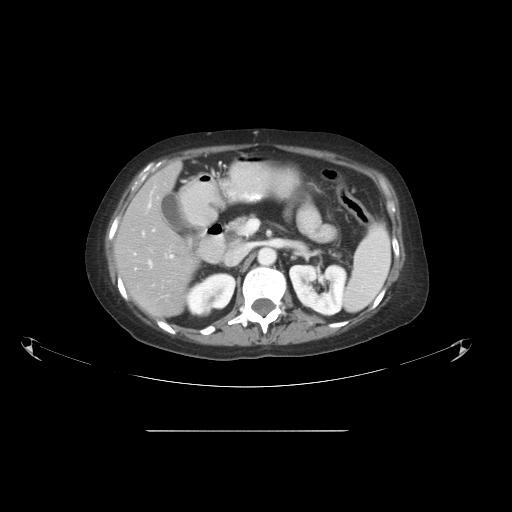
Contrast-enhanced abdominal CT, one axial slice. Slice 29 of 51 in the series (ordered by position). 120 kVp. Intravenous contrast given. Soft-tissue window (W 400 / L 40 HU). 5 mm slice thickness. 512 × 512 image matrix, field of view 475 × 475 mm. Female patient, age 48 years. From the clinical record (not read from this slice): diagnosis: colorectal cancer liver metastases, imaged before liver resection; multiple liver metastases: yes; largest metastasis: 1 cm.
Structures marked on this image (expert manual segmentation):
- hepatic veins: bounding box (x1, y1, x2, y2) in pixels: (148, 198, 173, 267)
- liver: (116, 163, 199, 317)
- planned liver remnant (the part of the liver to remain after resection): (116, 163, 199, 317)
- portal vein (with intrahepatic branches): (134, 192, 155, 270)